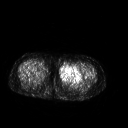
FDG PET of an extremity soft-tissue mass (from a PET/CT study), one axial slice; position 239 of 267 along the scan axis; 3.27 mm slice thickness; 128 × 128 image matrix. Female patient, age 42 years. From the clinical record (not read from this slice): histological type: pleiomorphic leiomyosarcoma; grade: intermediate; site of the primary tumour: left thigh.
Annotated regions visible in this slice (expert contour drawn on MRI and transferred to this co-registered scan by the dataset authors):
- gross tumour volume including surrounding oedema: bounding box <59,64,82,83> (left, top, right, bottom; pixels)
- gross tumour volume (mass): <59,64,82,83>